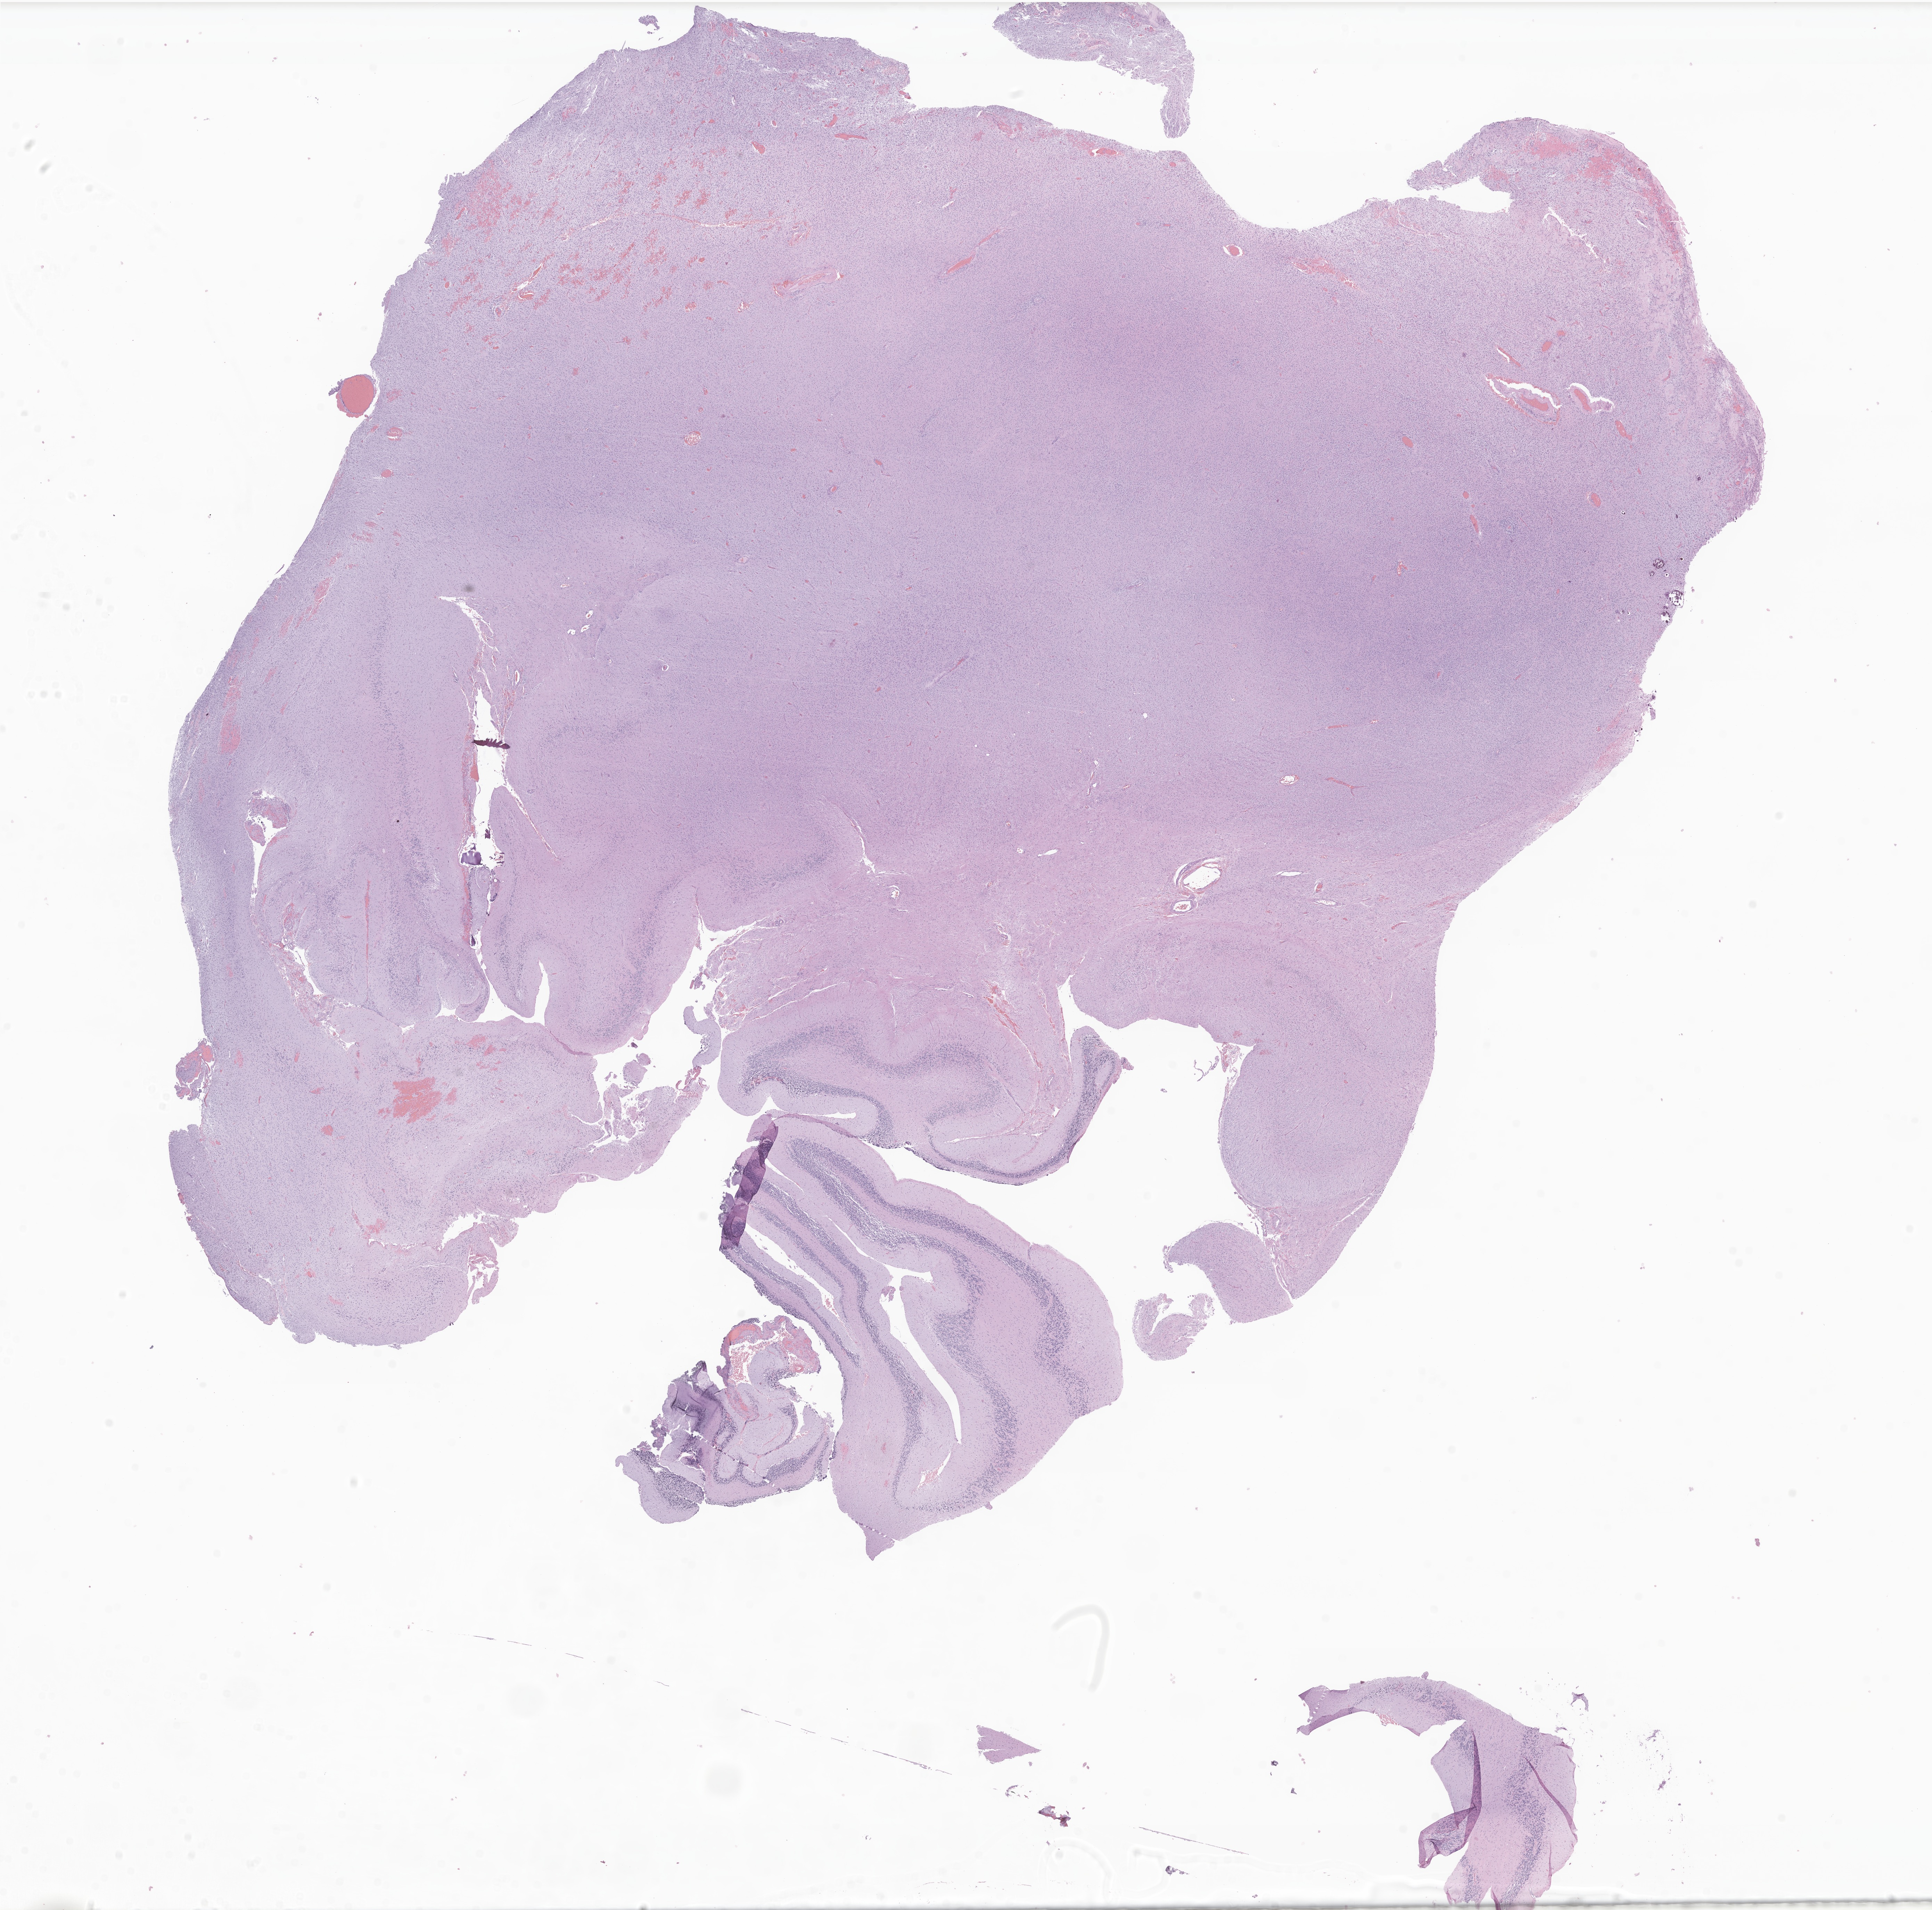
Digitized hematoxylin and eosin (H&E)-stained section of tumor tissue from the cerebellum, low-resolution overview of the scanned area, about 23.4 x 23.2 mm; formalin-fixed, paraffin-embedded (FFPE) tissue. Patient: male, age 218 months (18 years 2 months).
• diagnosis: Neoplasm, uncertain whether benign or malignant